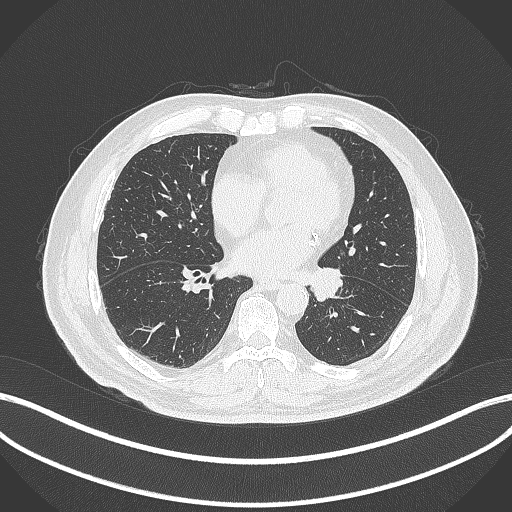
Chest CT, one axial slice; slice 120 of 312 in the series (ordered by position); reconstruction kernel B70f; 120 kVp; lung window (W 1500 / L -600 HU); 1 mm slice thickness; 512 × 512 image matrix. Patient: male, 71 years. From the clinical record (not read from this slice): clinical TNM (as recorded): T1b N0 M0.
Outlined on this slice (rectangle marked by the reading radiologist):
- lung tumour (recorded histology: squamous cell carcinoma): box from (x=307, y=267) to (x=346, y=301) px